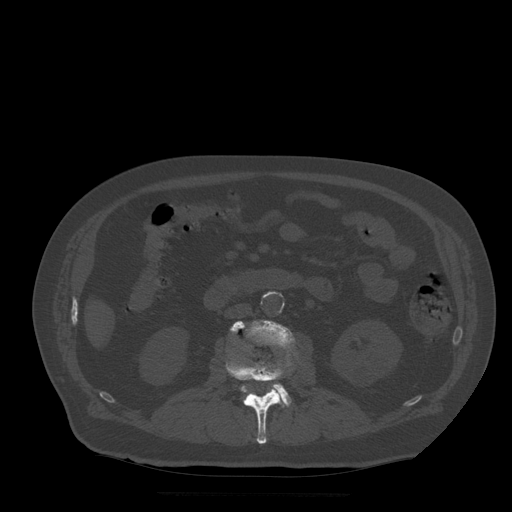
CT including the spine, one axial slice; position 159 of 522 along the scan axis; bone window (W 1800 / L 400 HU); 1.25 mm slice thickness; 512 × 512 image matrix. Patient age 72 years. From the clinical record (not read from this slice): primary cancer: prostate.
Outlined on this slice (semi-automatic segmentation, software-assisted and operator-edited):
- L2 vertebra: bounding box <226,356,286,444> (left, top, right, bottom; pixels)
- L3 vertebra: <231,321,295,406>